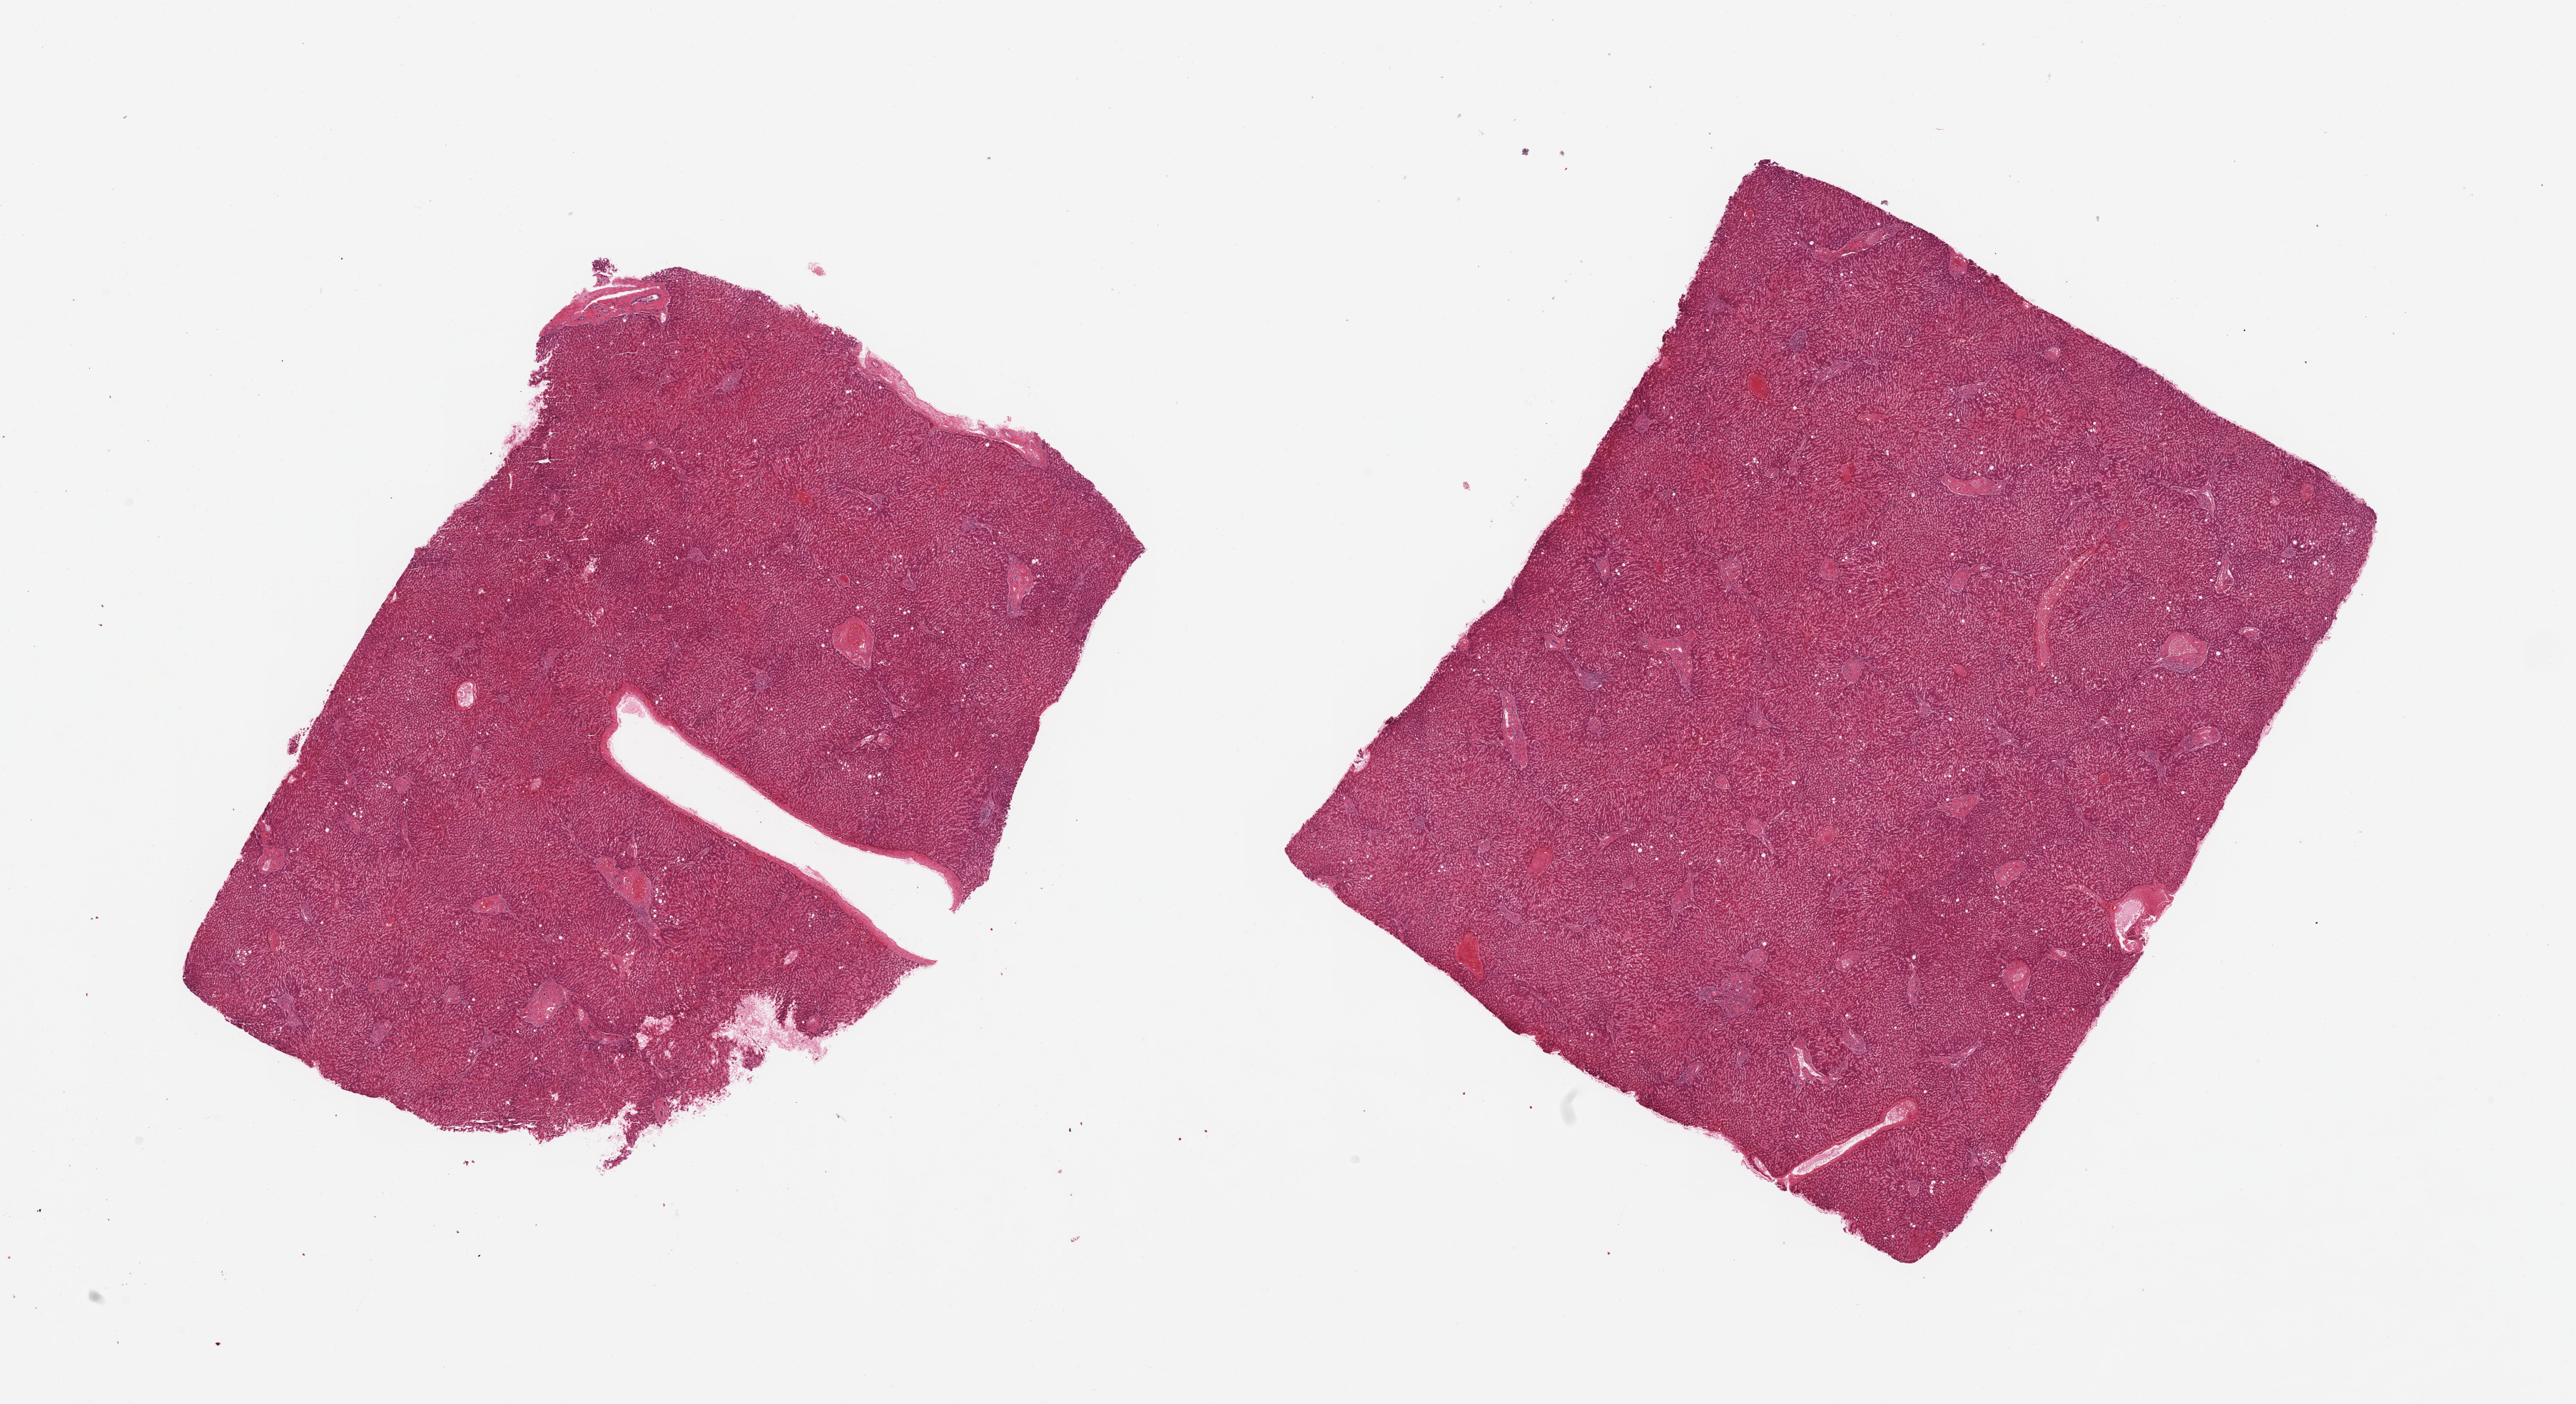
H&E whole-slide image, brightfield — whole scanned area (about 28.5 x 15.6 mm, slide scanned at 20x) shown as a low-resolution overview; PAXgene-fixed, paraffin-embedded tissue; sampled site (target tissue): liver; tissue donor sample. Donor: male.
- review note (as recorded): 2 pieces, mild passive congestion